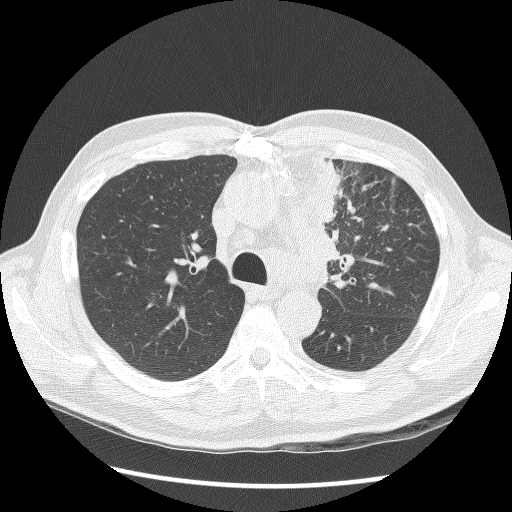
Chest CT (low-dose screening protocol), one axial image; second screening round (one year after baseline); lung window (W 1500 / L -600 HU); 2.5 mm slice thickness. Male participant, aged 64 years at enrolment. Former smoker at enrolment.
- Lesion marked by an expert reader, bounding box <298,163,372,289> (left, top, right, bottom; pixels).
- No non-calcified nodule or mass ≥4 mm was recorded by the screening reader at this exam.